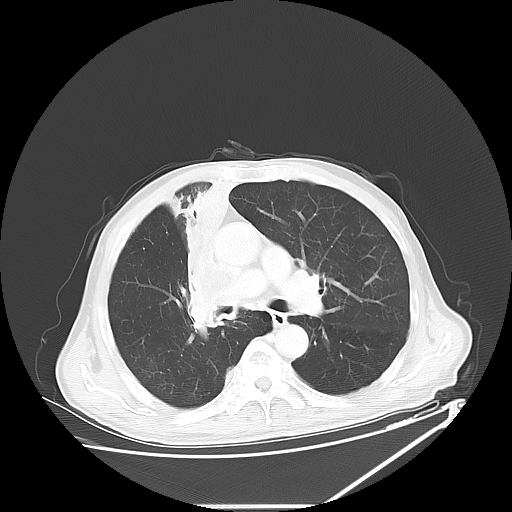
Chest CT, one axial slice. Slice 38 of 60 in the series (ordered by position). Reconstruction kernel LUNG. 120 kVp. Lung window (W 1500 / L -600 HU). 512 × 512 image matrix. Patient: male, 73 years. From the clinical record (not read from this slice): clinical TNM (as recorded): T2a N1 M0.
Annotated regions visible in this slice (bounding box drawn by a radiologist):
- lung tumour (recorded histology: squamous cell carcinoma): box from (x=176, y=181) to (x=252, y=339) px